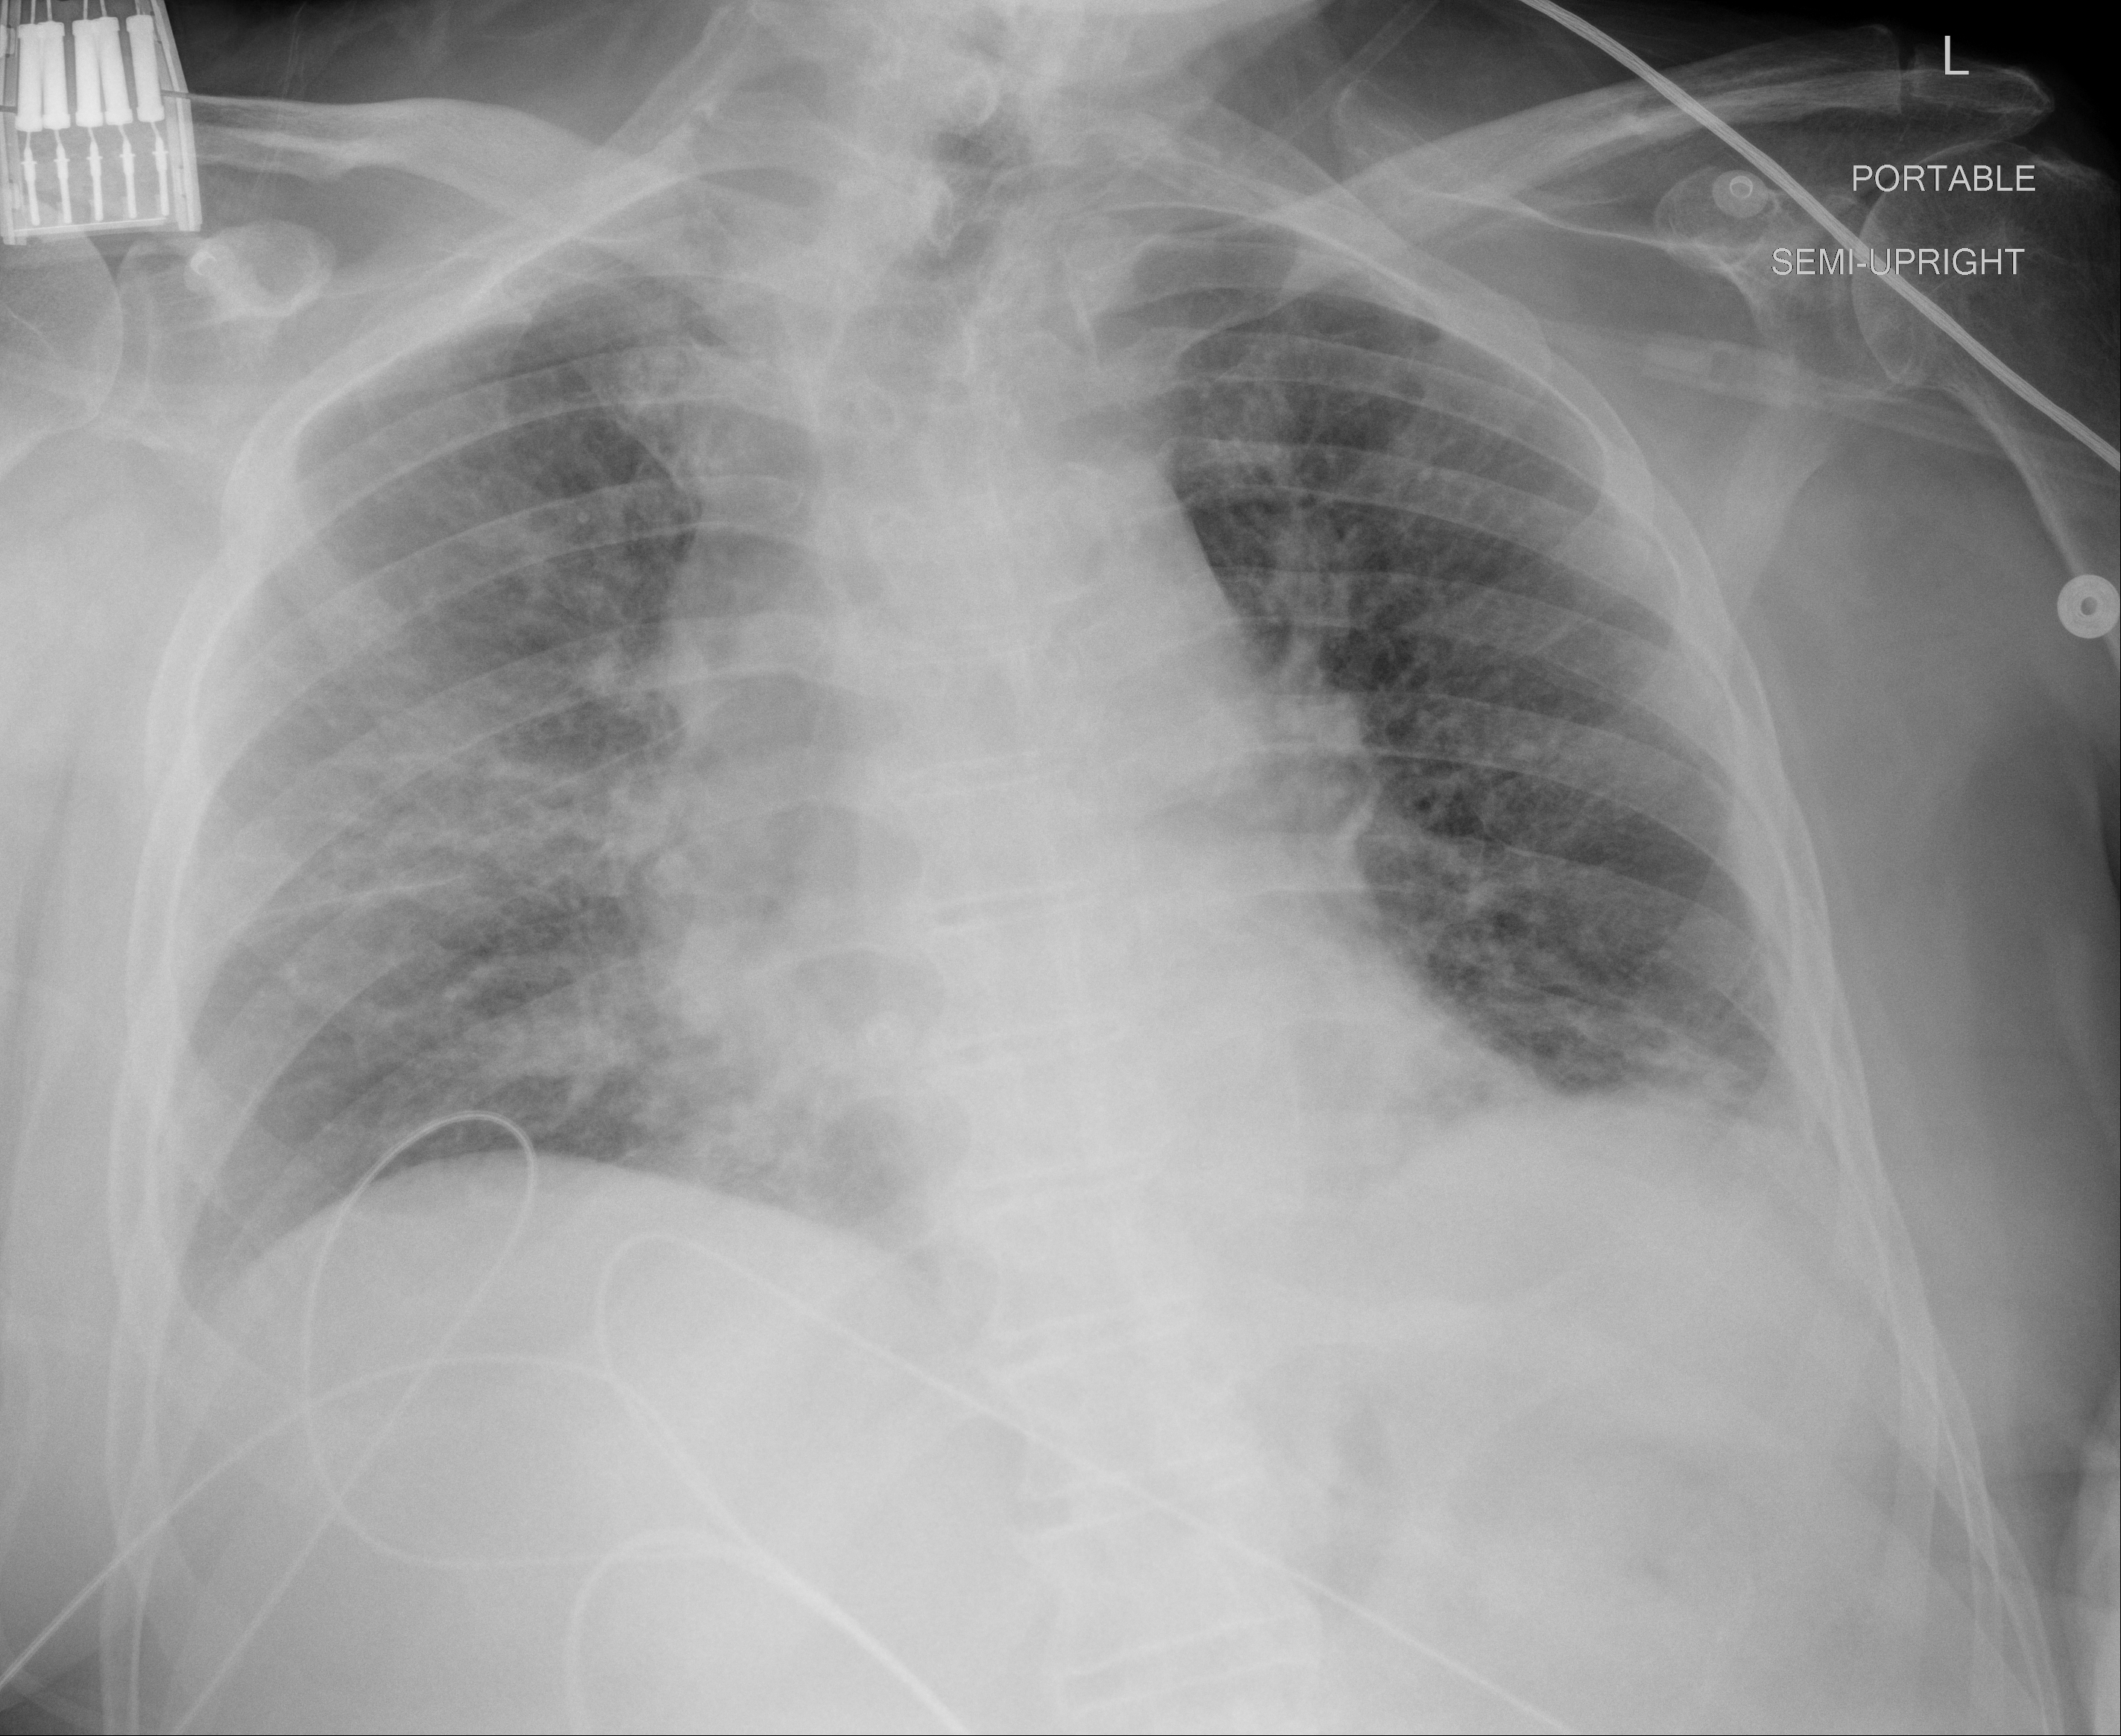
Chest X-ray, AP projection. Male patient, age 89 years; imaged 1 day after the COVID-19 diagnosis.
Key findings recorded by the radiologist: slightly increased interstitial opacities noted bilaterally.